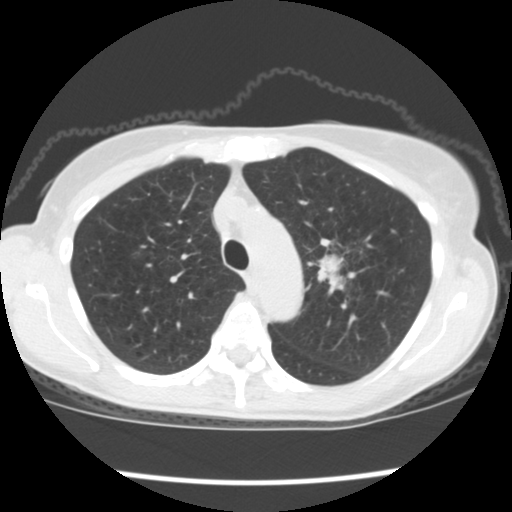
Low-dose screening chest CT, one axial slice. Position 136 of 176 along the scan axis. Reconstruction kernel STANDARD. 120 kVp. Lung window (W 1500 / L -600 HU). 2.5 mm slice thickness. 512 × 512 image matrix.
Structures marked on this image (manually delineated by an expert):
- lesion 1 (tumor, upper lobe of left lung): box from (x=318, y=255) to (x=355, y=293) px